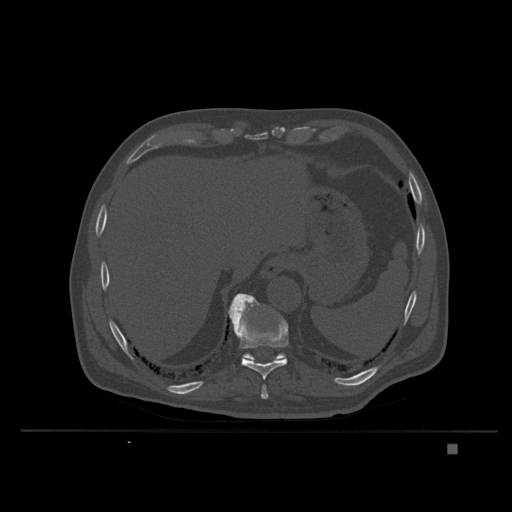
CT including the spine, one axial slice. Slice 192 of 435 in the series (ordered by position). Bone window (W 1800 / L 400 HU). 1.5 mm slice thickness. 512 × 512 image matrix, field of view 434 × 434 mm. Patient: male, 73 years. Case-level facts recorded for this patient, not image findings: primary cancer: skin.
Annotated regions visible in this slice (semi-automatically segmented with operator editing):
- T10 vertebra: bounding box <232,307,289,380> (left, top, right, bottom; pixels)
- T11 vertebra: <228,293,288,363>
- T9 vertebra: <261,385,269,401>